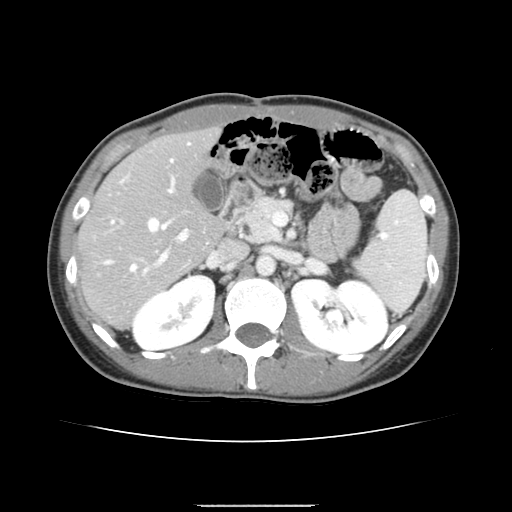
Contrast-enhanced abdominal CT, one axial slice; 120 kVp; intravenous contrast given; soft-tissue window (W 400 / L 40 HU); 2.5 mm slice thickness; 512 × 512 image matrix, field of view 324 × 324 mm. Female patient, age 32 years. Case-level facts recorded for this patient, not image findings: diagnosis: colorectal cancer liver metastases, imaged before liver resection; multiple liver metastases: yes; largest metastasis: 0.7 cm; chemotherapy before resection: yes.
Structures marked on this image (manually delineated by an expert):
- hepatic veins: bounding box [x1, y1, x2, y2] px = [106, 159, 173, 270]
- liver: [79, 130, 224, 326]
- planned liver remnant (the part of the liver to remain after resection): [79, 130, 223, 276]
- portal vein (with intrahepatic branches): [122, 176, 188, 272]
- liver metastasis: [142, 281, 147, 286]